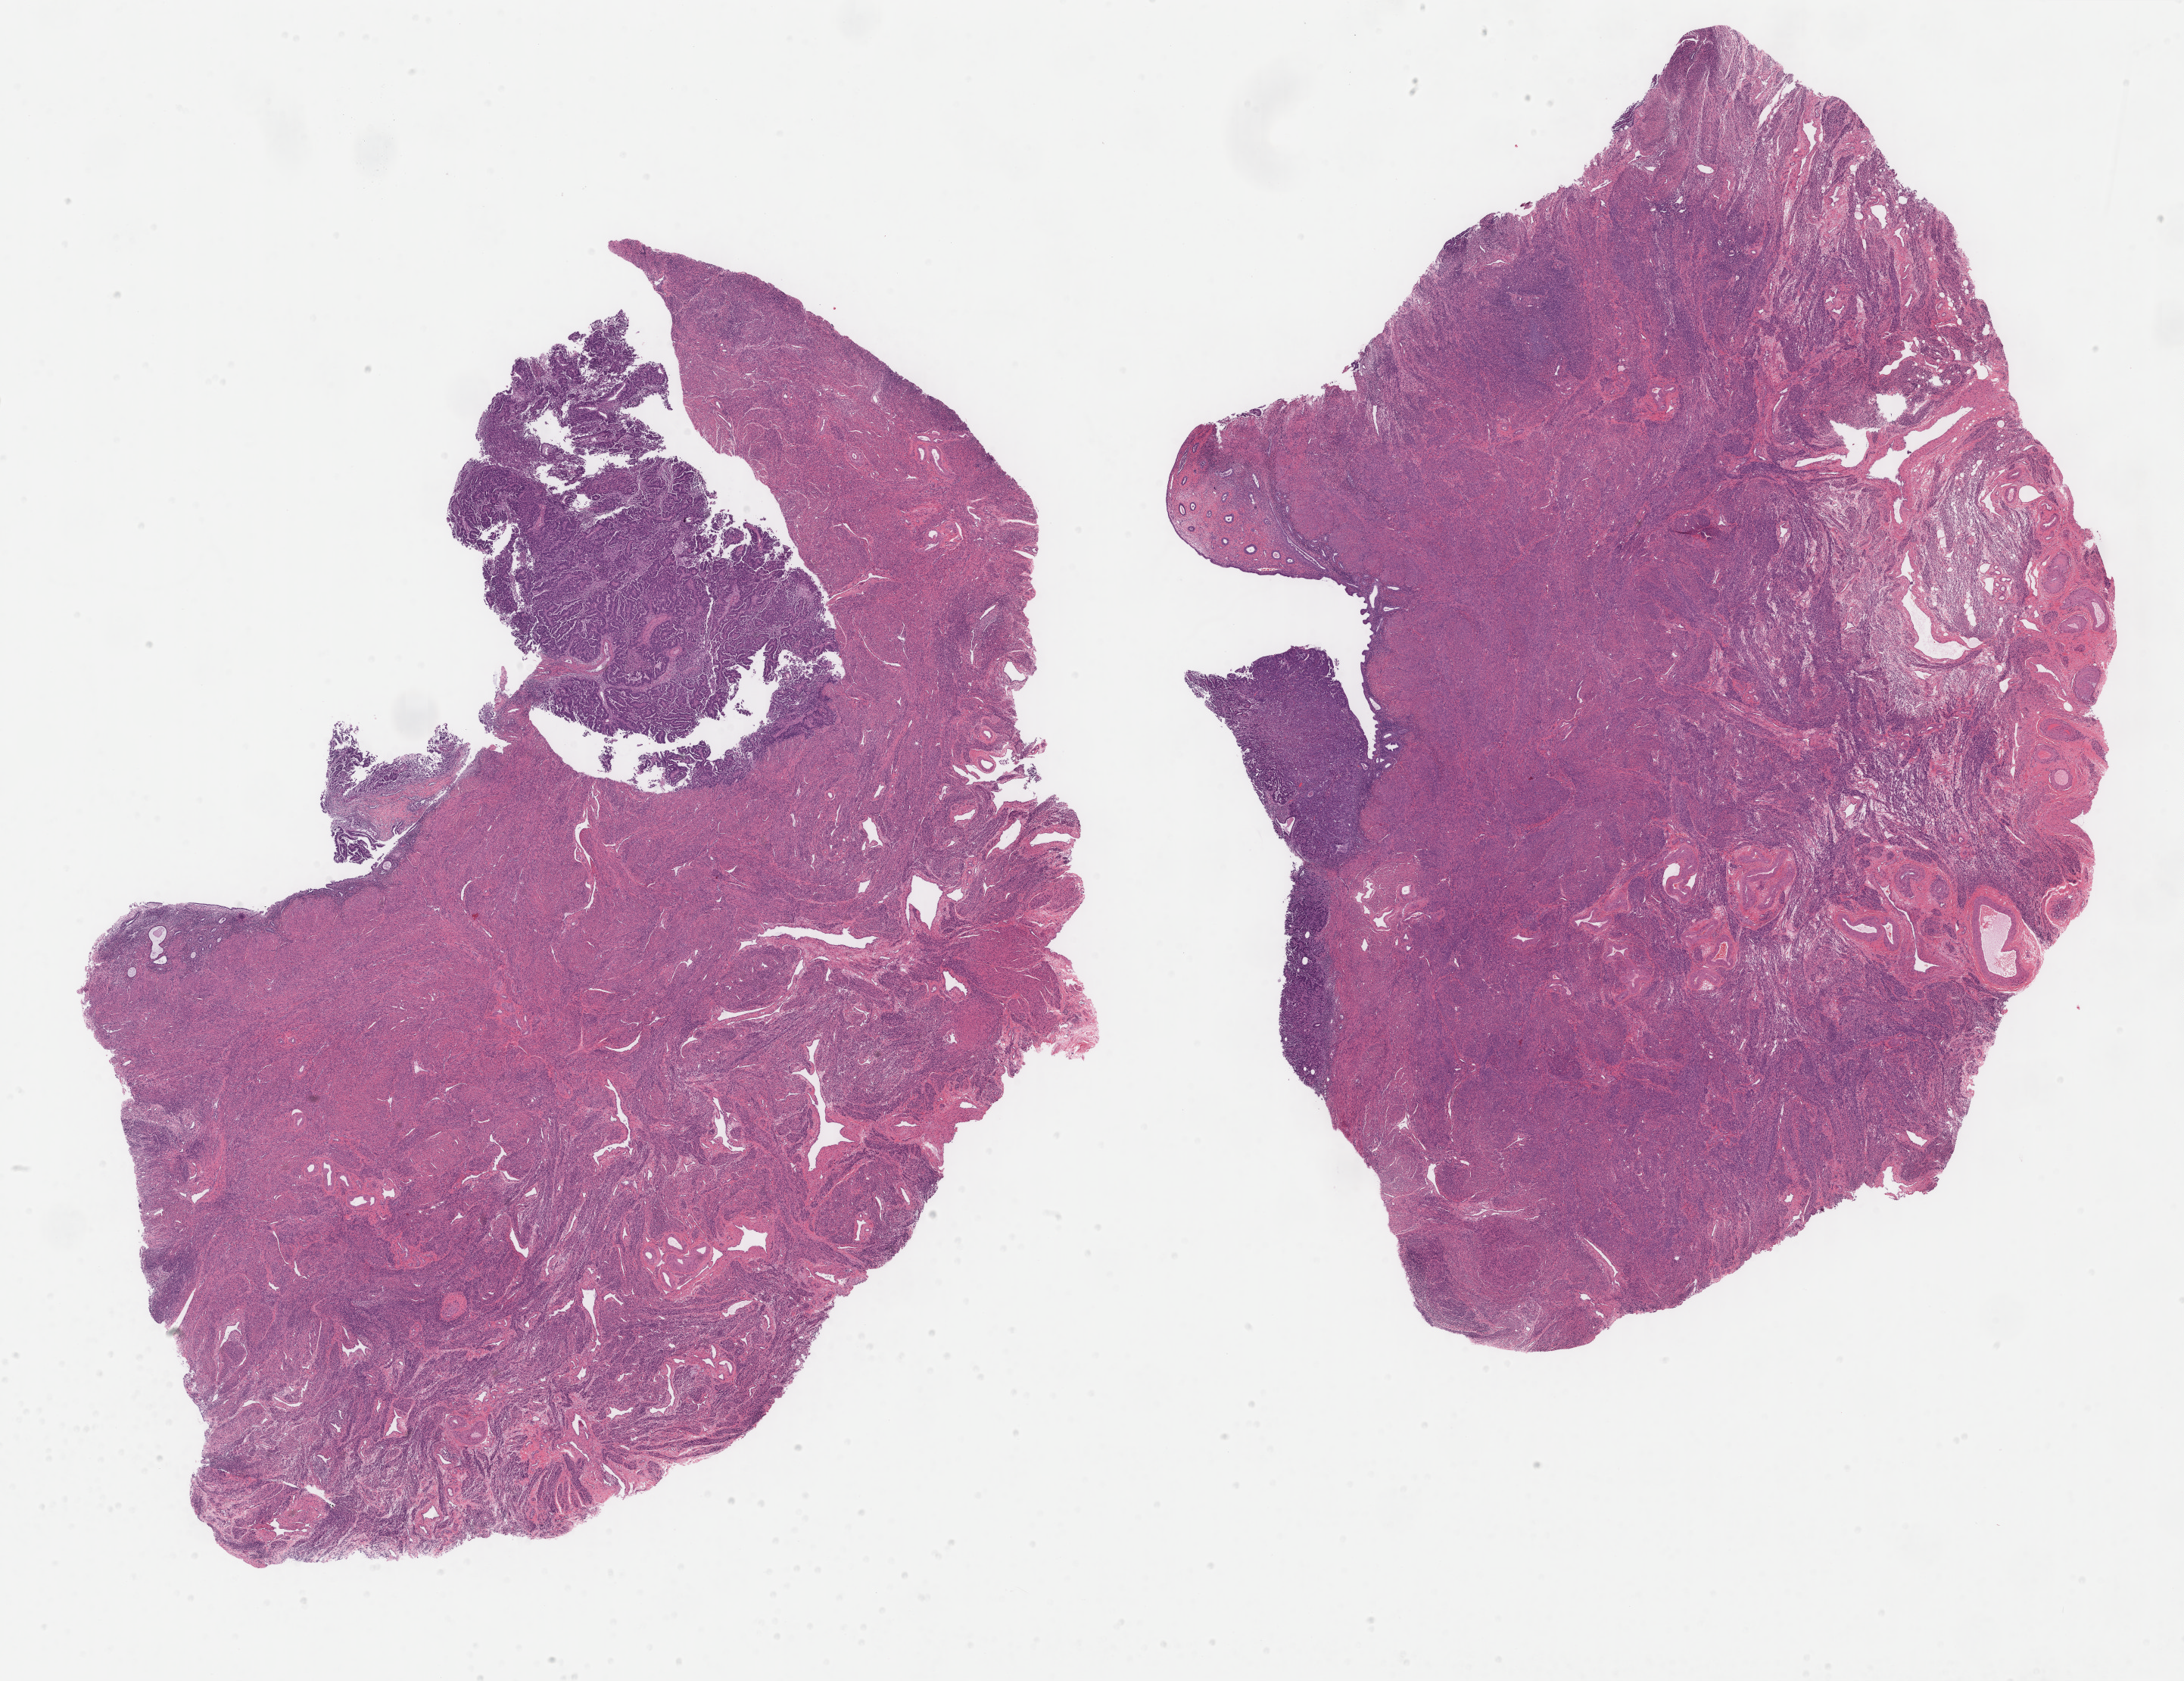
H&E-stained whole-slide image — shown as a low-resolution overview of the whole scanned area (about 22.9 x 17.6 mm), formalin-fixed paraffin-embedded (FFPE) diagnostic section, primary tumour sample from the uterus. Female, age 62 years at initial diagnosis. Histologic grade: high grade.
Diagnosis: Serous cystadenocarcinoma, NOS. Lymph nodes positive (case pathology): 0 of 22 examined. FIGO stage: IC.